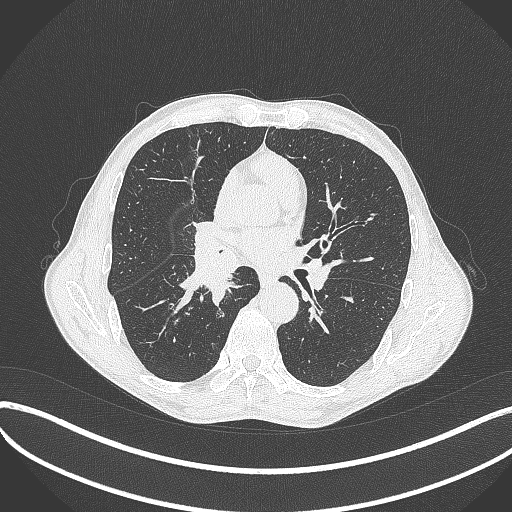
Chest CT, one axial slice. Lung window (W 1500 / L -600 HU). 1 mm slice thickness. 512 × 512 image matrix, field of view 400 × 400 mm. Patient: male, 65 years. Case-level facts recorded for this patient, not image findings: clinical TNM (as recorded): T2a N0 M0.
Annotated regions visible in this slice (bounding box drawn by a radiologist):
- lung tumour (recorded histology: squamous cell carcinoma): bounding box [x1, y1, x2, y2] px = [185, 214, 240, 307]